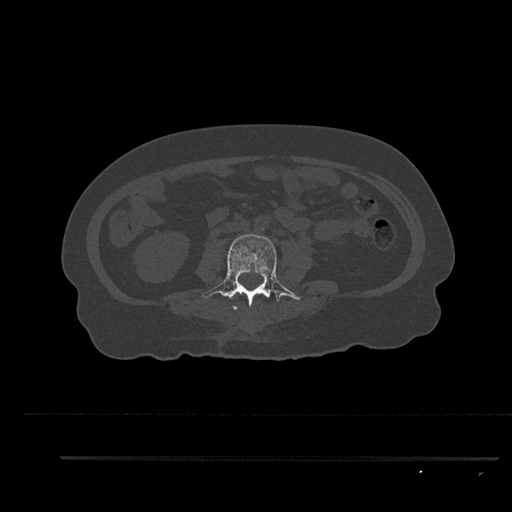
CT including the spine, one axial slice; slice 92 of 797 in the series (ordered by position); 120 kVp; bone window (W 1800 / L 400 HU); 0.5 mm slice thickness; 512 × 512 image matrix, field of view 408 × 408 mm. Patient: female, 44 years. From the clinical record (not read from this slice): primary cancer: renal; vertebrae with lytic lesions (as recorded): L1.
Annotated regions visible in this slice (semi-automatic segmentation, software-assisted and operator-edited):
- L2 vertebra: bounding box (x1, y1, x2, y2) in pixels: (233, 306, 238, 310)
- L3 vertebra: (202, 234, 301, 310)